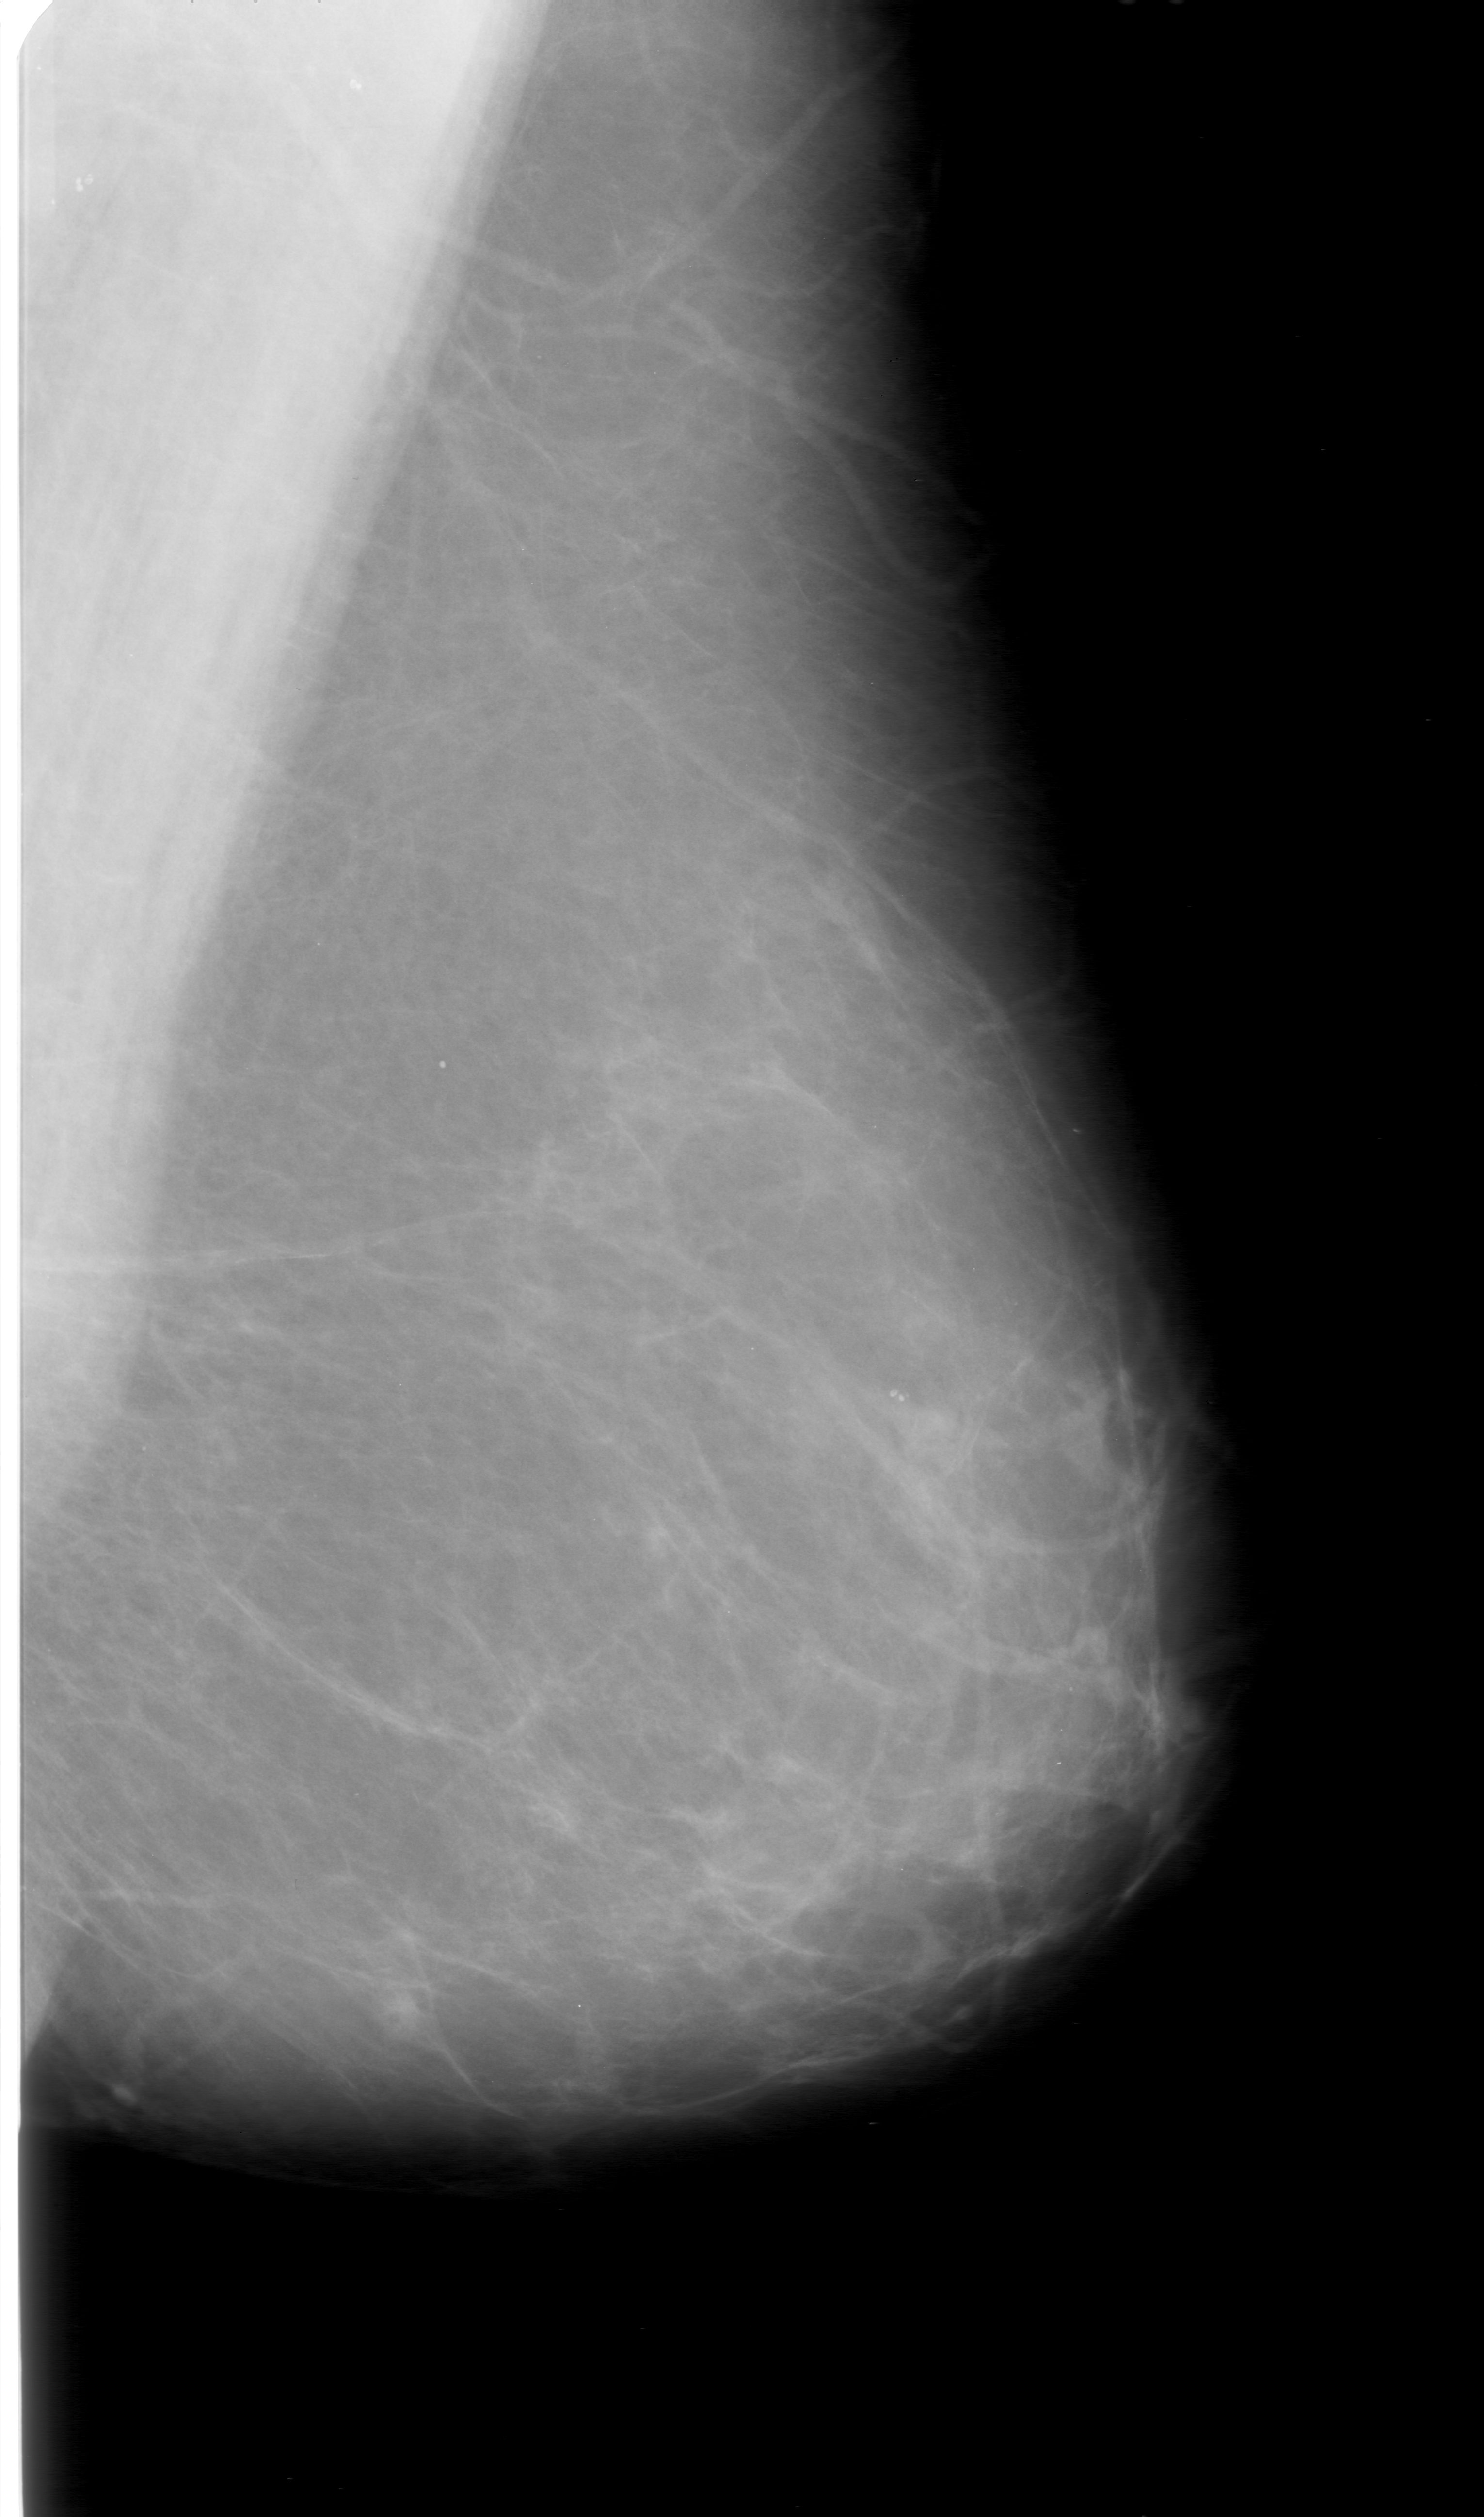
Mammogram (digitized film), left breast, mediolateral oblique (MLO) view, BI-RADS breast density category 1 (scale 1–4).
Finding: mass, shape lobulated, margins obscured; BI-RADS assessment category 0 (incomplete: needs additional imaging); subtlety rating 4 on a 1 (subtle) to 5 (obvious) scale; pathology (as recorded): malignant.